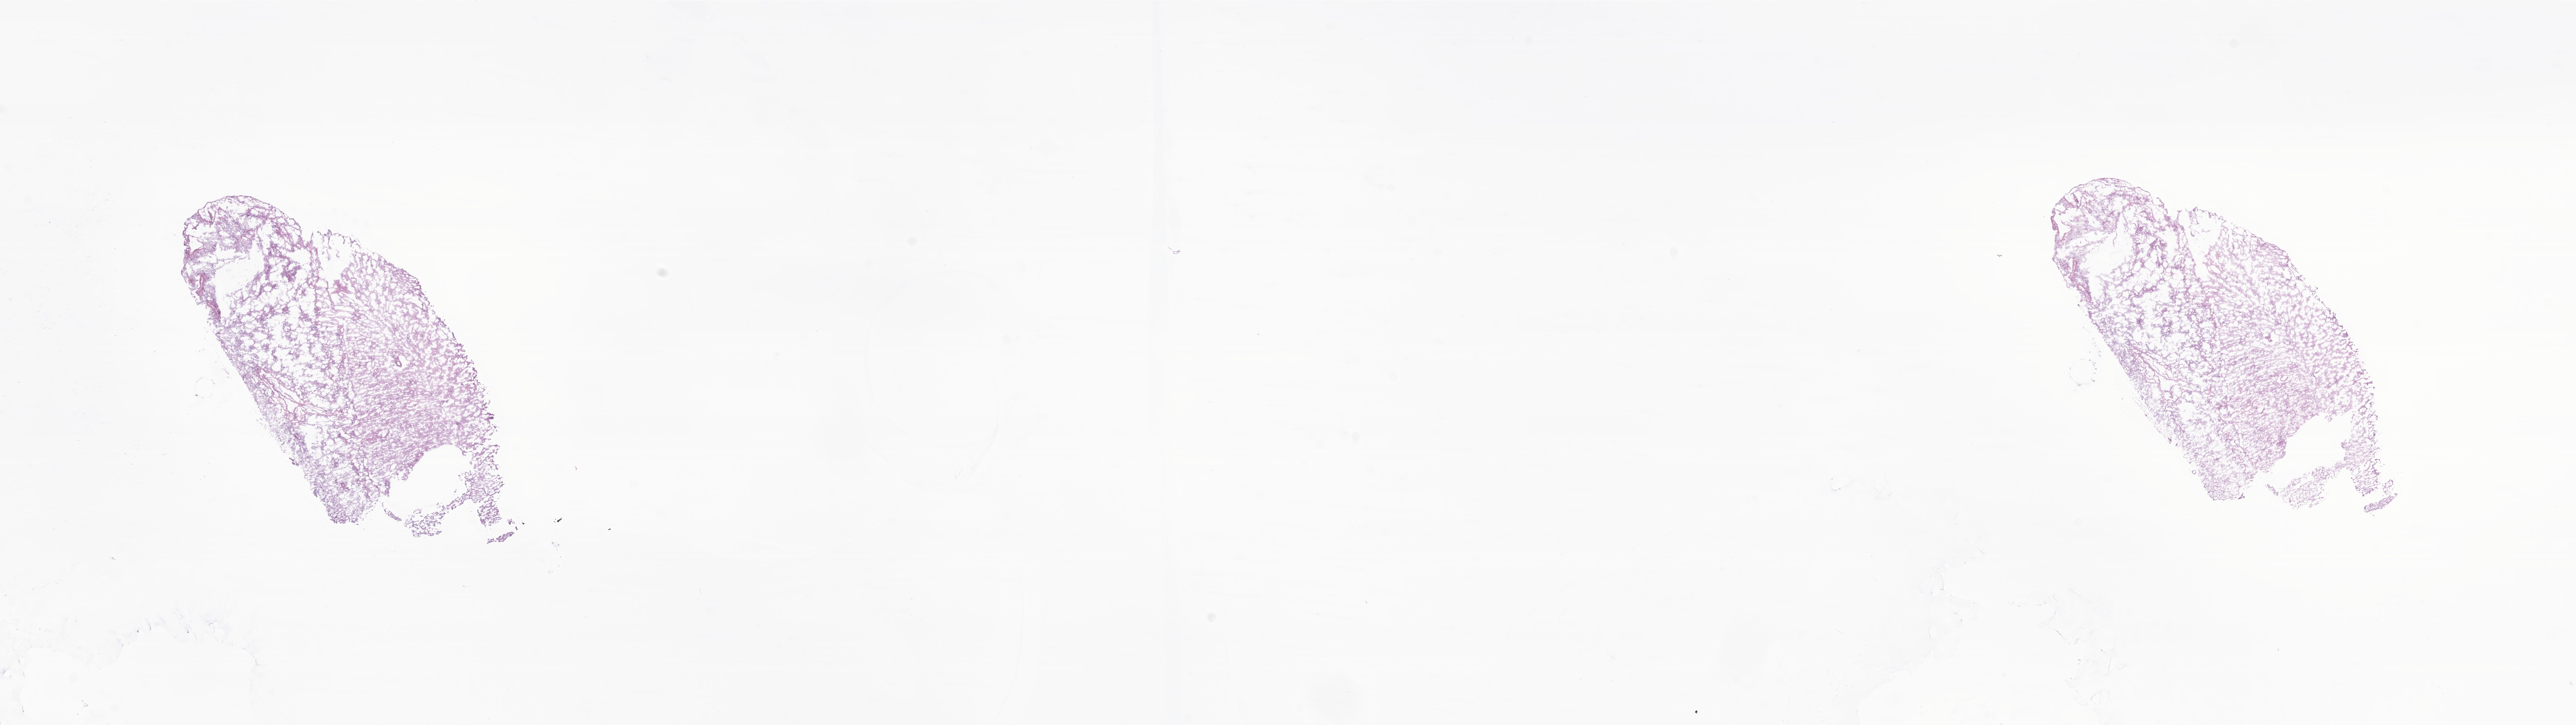
Hematoxylin and eosin (H&E) whole-slide image of tumor tissue from the brain — a low-resolution overview of the entire scanned area, about 26.6 x 7.5 mm. Cryosection (OCT / tissue freezing medium). Patient: female, age 104 months (8 years 8 months).
Recorded diagnosis: Pilocytic astrocytoma.